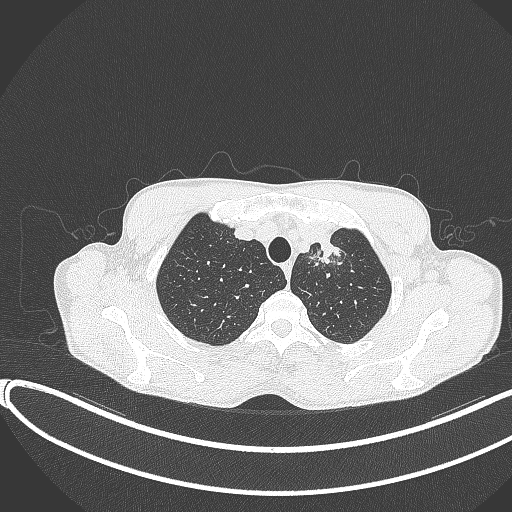
Chest CT, one axial slice. Slice 330 of 374 in the series (ordered by position). Reconstruction kernel B70f. 120 kVp. Lung window (W 1500 / L -600 HU). 512 × 512 image matrix, field of view 400 × 400 mm. Patient: male, 58 years. Case-level facts recorded for this patient, not image findings: clinical TNM (as recorded): T1c N1 M0.
Outlined on this slice (bounding box drawn by a radiologist):
- lung tumour (recorded histology: adenocarcinoma): bounding box [x1, y1, x2, y2] px = [302, 226, 348, 272]